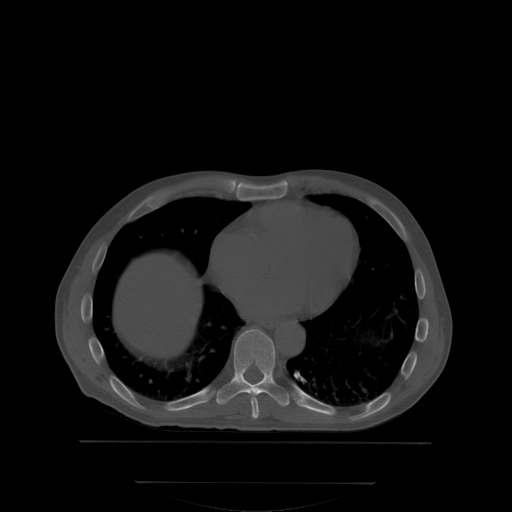
CT including the spine, one axial slice. Position 206 of 350 along the scan axis. Bone window (W 1800 / L 400 HU). 2.5 mm slice thickness. 512 × 512 image matrix, field of view 500 × 500 mm. Male patient, age 58 years. Case-level facts recorded for this patient, not image findings: primary cancer: prostate.
Outlined on this slice (semi-automatic segmentation, software-assisted and operator-edited):
- T8 vertebra: bounding box [x1, y1, x2, y2] px = [251, 395, 260, 417]
- T9 vertebra: [216, 329, 300, 406]